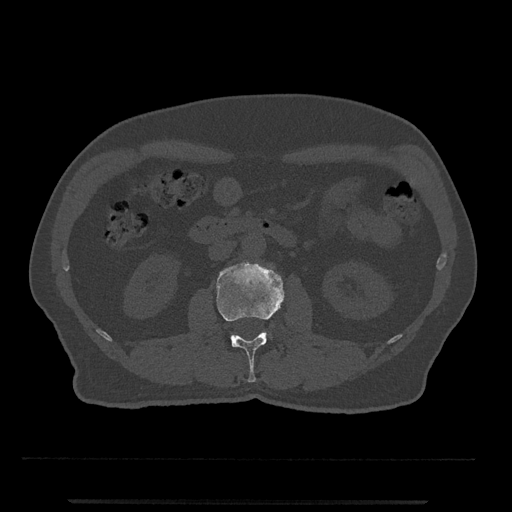
CT including the spine, one axial slice; slice 255 of 797 in the series (ordered by position); reconstruction kernel Br40s/3; 120 kVp; bone window (W 1800 / L 400 HU); 512 × 512 image matrix, field of view 419 × 419 mm. Male patient, age 63 years. From the clinical record (not read from this slice): primary cancer: prostate.
Annotated regions visible in this slice (semi-automatic segmentation, software-assisted and operator-edited):
- L2 vertebra: bounding box <217,262,285,382> (left, top, right, bottom; pixels)